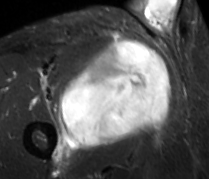
MRI of an extremity soft-tissue mass, one axial slice. Slice 54 of 89 in the series (ordered by position). STIR. MR volume resampled by the dataset authors to the PET/CT grid (not the native acquisition matrix). 3.27 mm slice thickness. 209 × 179 image matrix. Male patient. Case-level facts recorded for this patient, not image findings: histological type: undifferentiated - pleiomorphic; grade: high; site of the primary tumour: right thigh.
Outlined on this slice (expert contour drawn on MRI and transferred to this co-registered scan by the dataset authors):
- gross tumour volume including surrounding oedema: box from (x=57, y=39) to (x=170, y=150) px
- gross tumour volume (mass): (x=60, y=39)–(x=170, y=149)